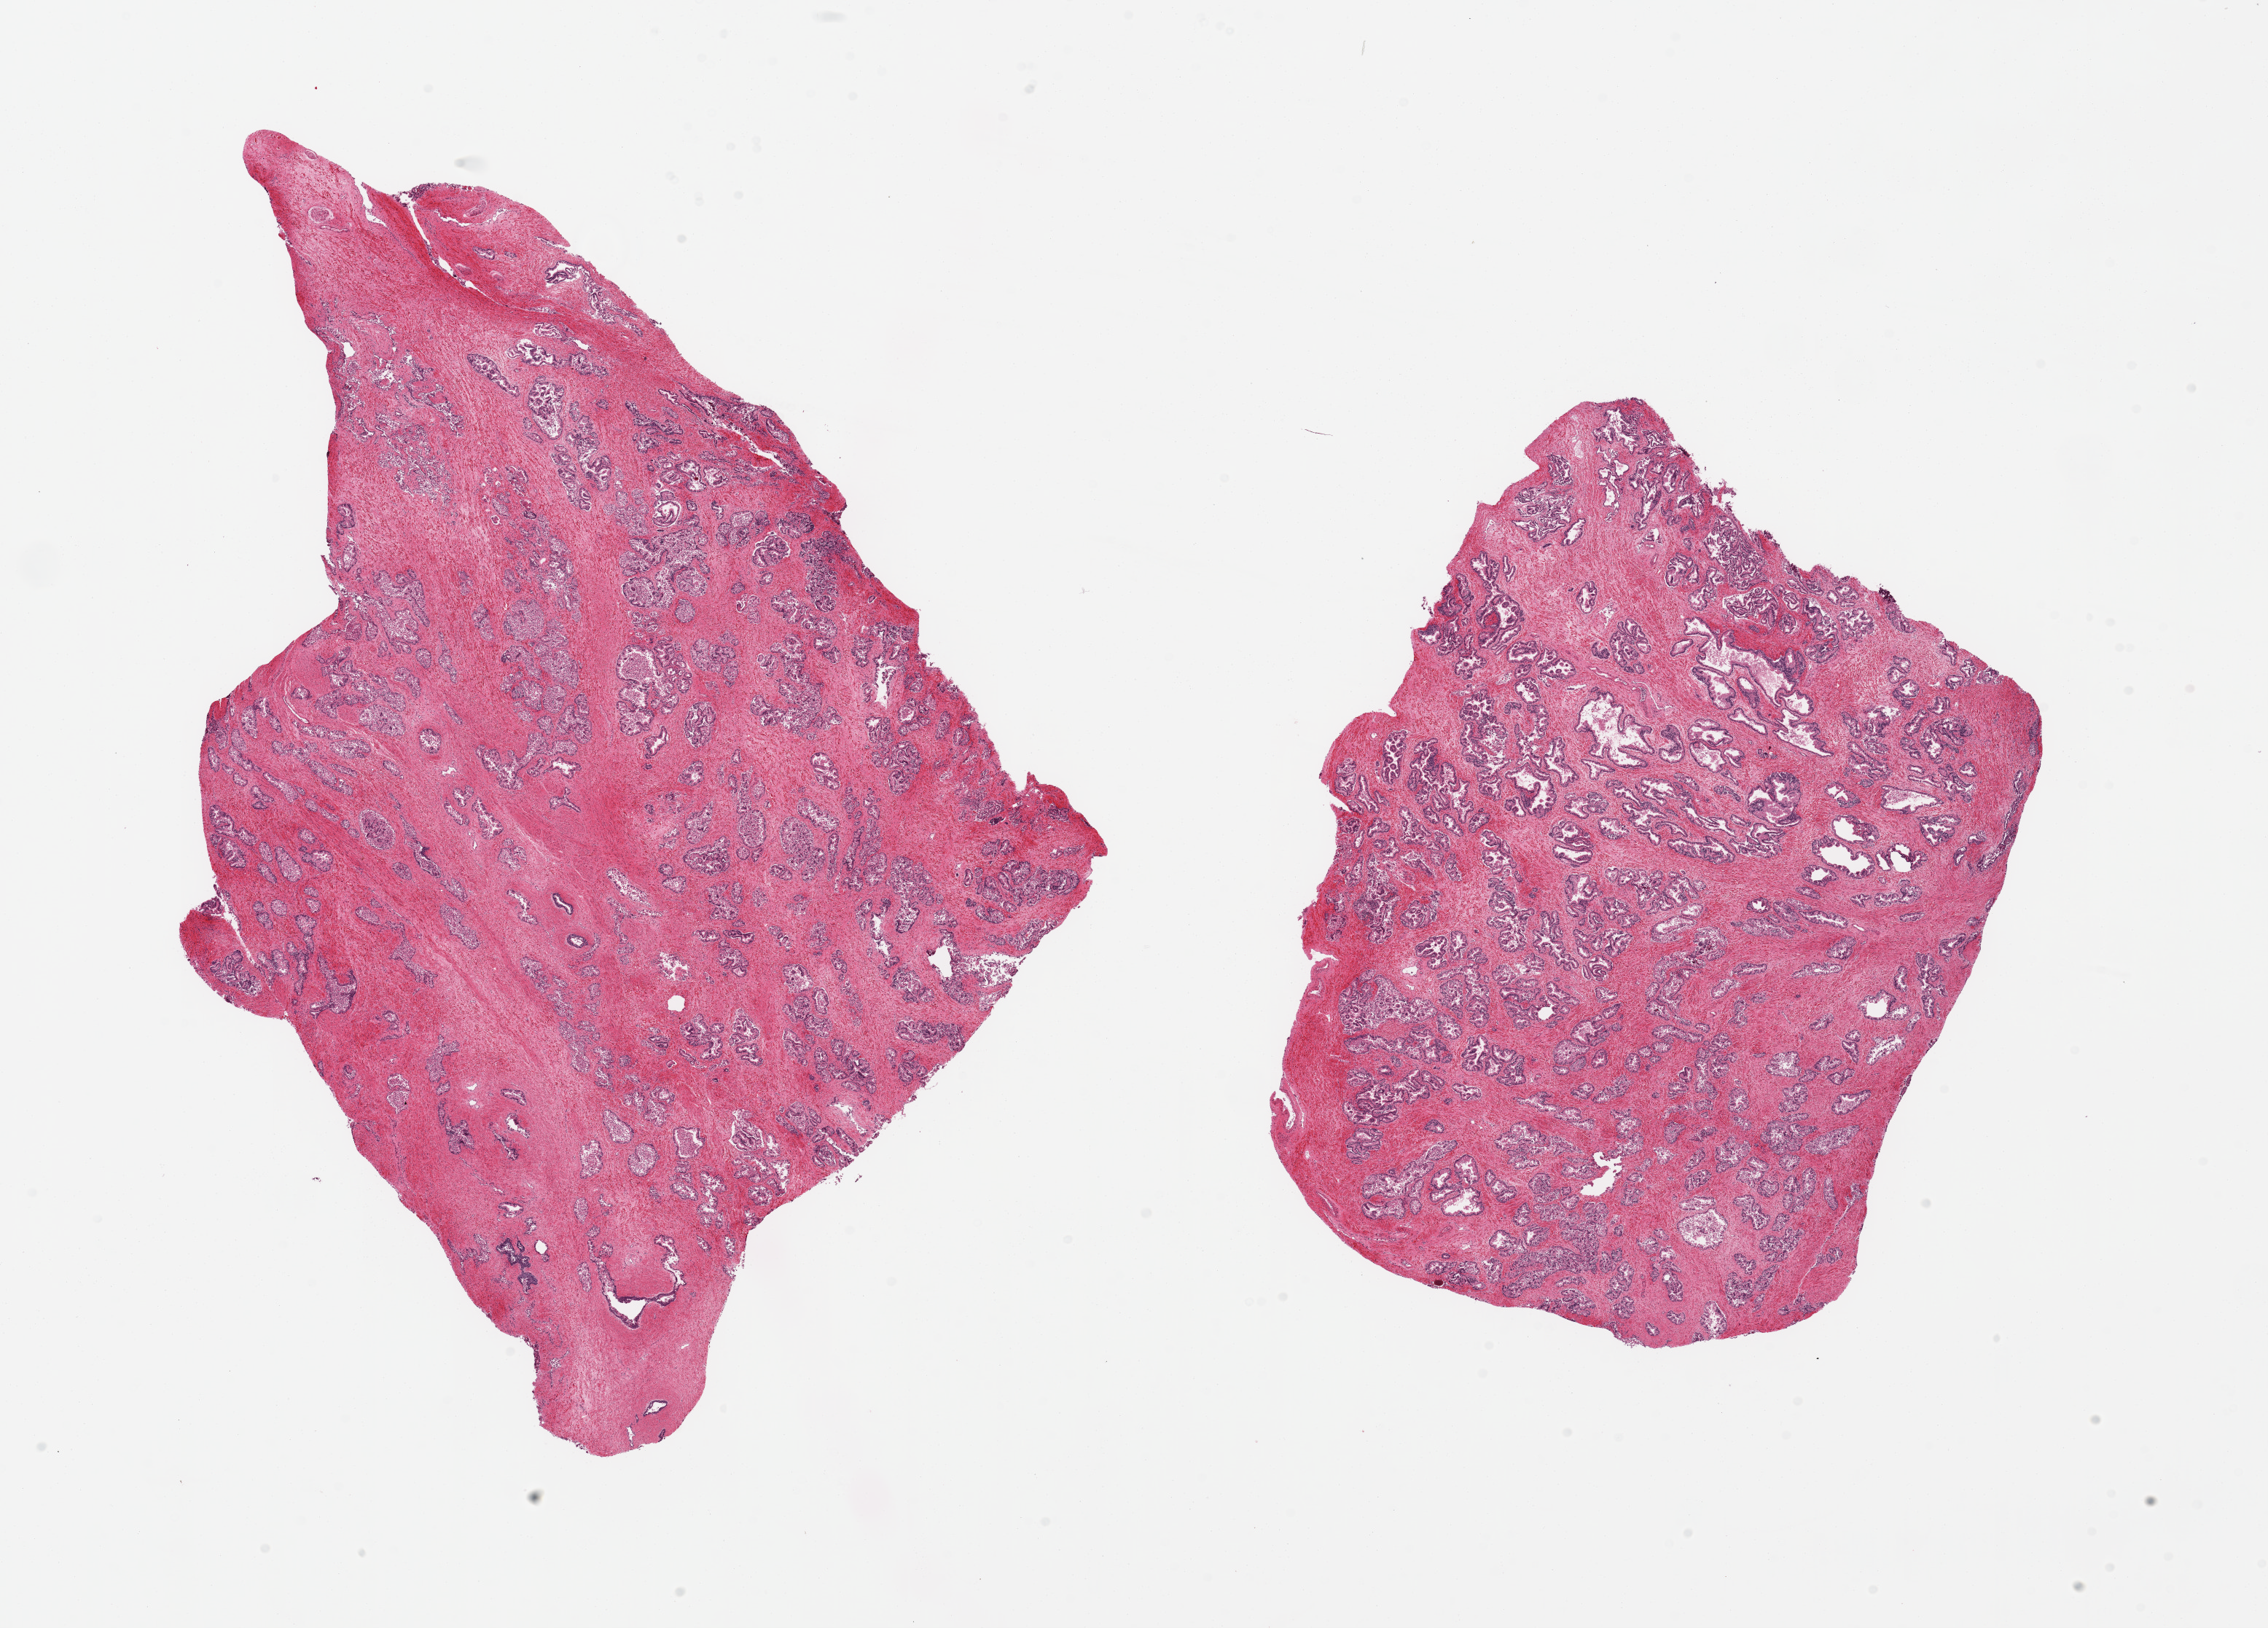
Hematoxylin and eosin (H&E) whole-slide image, brightfield — a low-resolution overview of the entire scanned area, about 24.6 x 17.7 mm (slide scanned at 20x); PAXgene-fixed, paraffin-embedded tissue; section of prostate (target tissue); donor tissue sample.
Reviewer comment on this tissue sample: 2 pieces; variable acinar autolysis, moderate to severe.